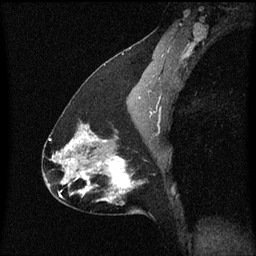
Breast MRI (dynamic contrast-enhanced), one sagittal slice; position 34 of 60 along the scan axis; dynamic contrast-enhanced series, image 2 of 3 at this slice position (ordered by acquisition); 1.5 T; TE 4.2 ms, TR 8.4 ms; 256 × 256 image matrix, field of view 200 × 200 mm. Female patient, age 47 years.
Structures marked on this image (semi-automatically segmented with operator editing):
- analysis volume of interest (the breast-tissue region the enhancement analysis was run in; not a lesion): bounding box (x1, y1, x2, y2) in pixels: (81, 138, 143, 215)
- tumour enhancement mask (voxels above the 70 % enhancement threshold inside the analysis volume of interest): (81, 138, 134, 201)